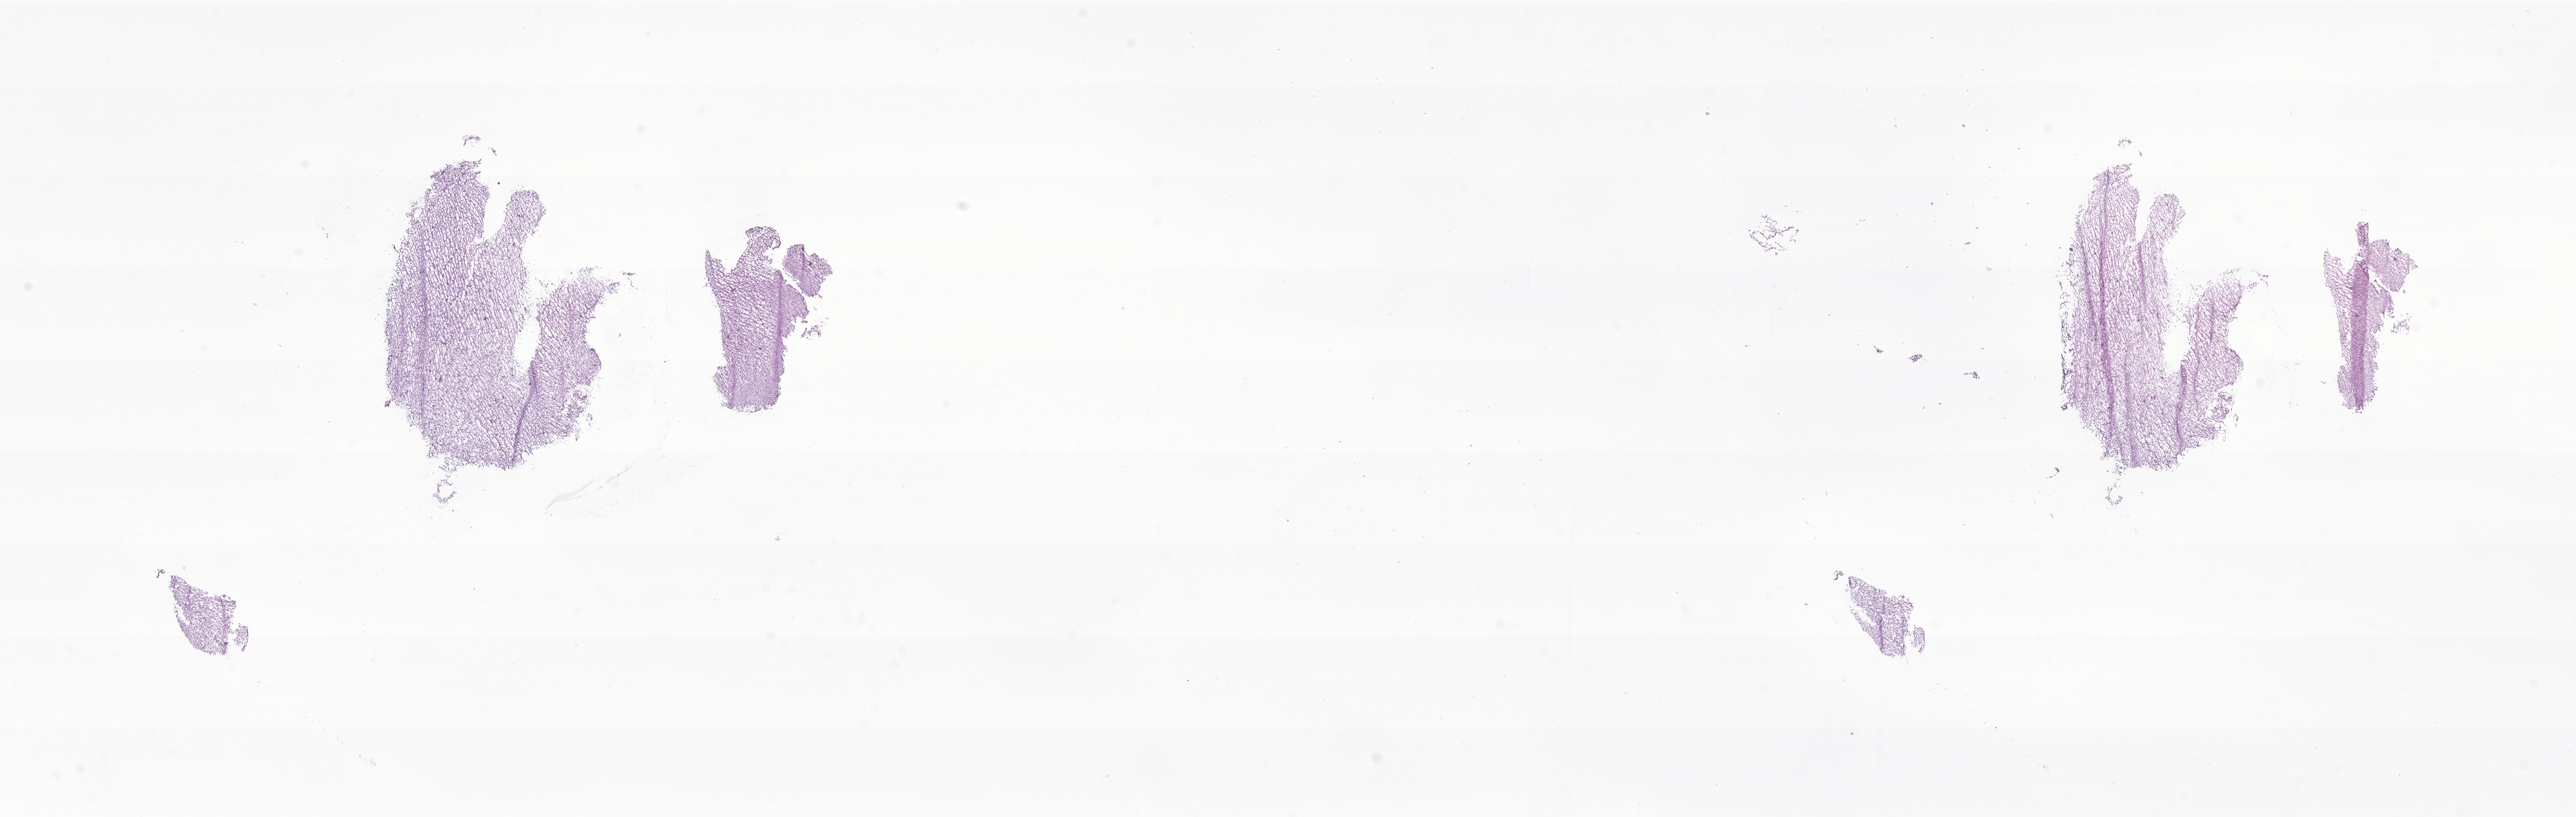
Whole-slide image, hematoxylin and eosin (H&E) stain of tumor tissue from the brain — low-resolution overview of the scanned area, about 29.9 x 9.5 mm; frozen section (OCT-embedded). Male patient, age 112 months (9 years 4 months).
* diagnosis: Neoplasm, malignant